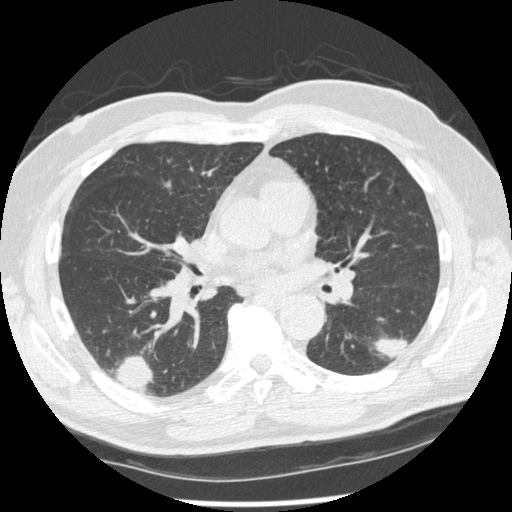
Axial slice from a low-dose chest CT screening exam; second annual screen; lung window (W 1500 / L -600 HU); 120 kVp; slice 119 of 227 in the series; 512 × 512 image matrix, field of view 360 × 360 mm. Male, age 74 years at enrolment.
• Lesion marked by an expert reader, box from (x=368, y=314) to (x=423, y=368) px.
• The screening reader recorded 7 non-calcified nodules or masses ≥4 mm on this exam (right upper lobe, right lower lobe, right upper lobe, right lower lobe, left lower lobe, left upper lobe, left upper lobe); which of them this box marks is not recorded.
• Official screen result: positive, other.
• Participant outcome: lung cancer diagnosed 43 days after this screen — squamous cell carcinoma, NOS, left lower lobe, well differentiated (G1), stage IA (AJCC 6th edition), 28 mm at pathology.